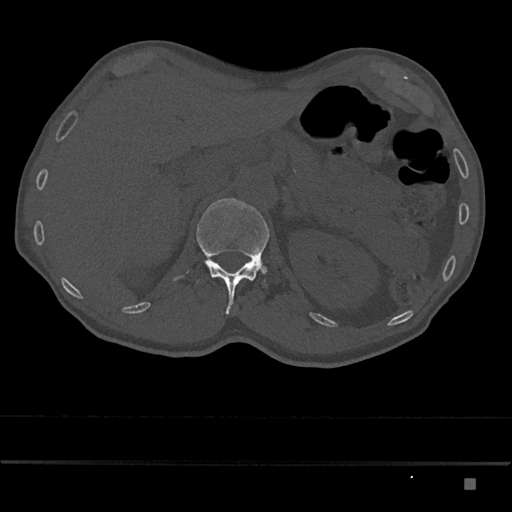
CT including the spine, one axial slice. Position 544 of 797 along the scan axis. Reconstruction kernel Br40s/3. 120 kVp. Bone window (W 1800 / L 400 HU). 0.5 mm slice thickness. 512 × 512 image matrix, field of view 390 × 390 mm. Male patient, age 72 years. From the clinical record (not read from this slice): primary cancer: prostate.
Structures marked on this image (semi-automatic segmentation, software-assisted and operator-edited):
- L1 vertebra: box from (x=197, y=198) to (x=270, y=315) px